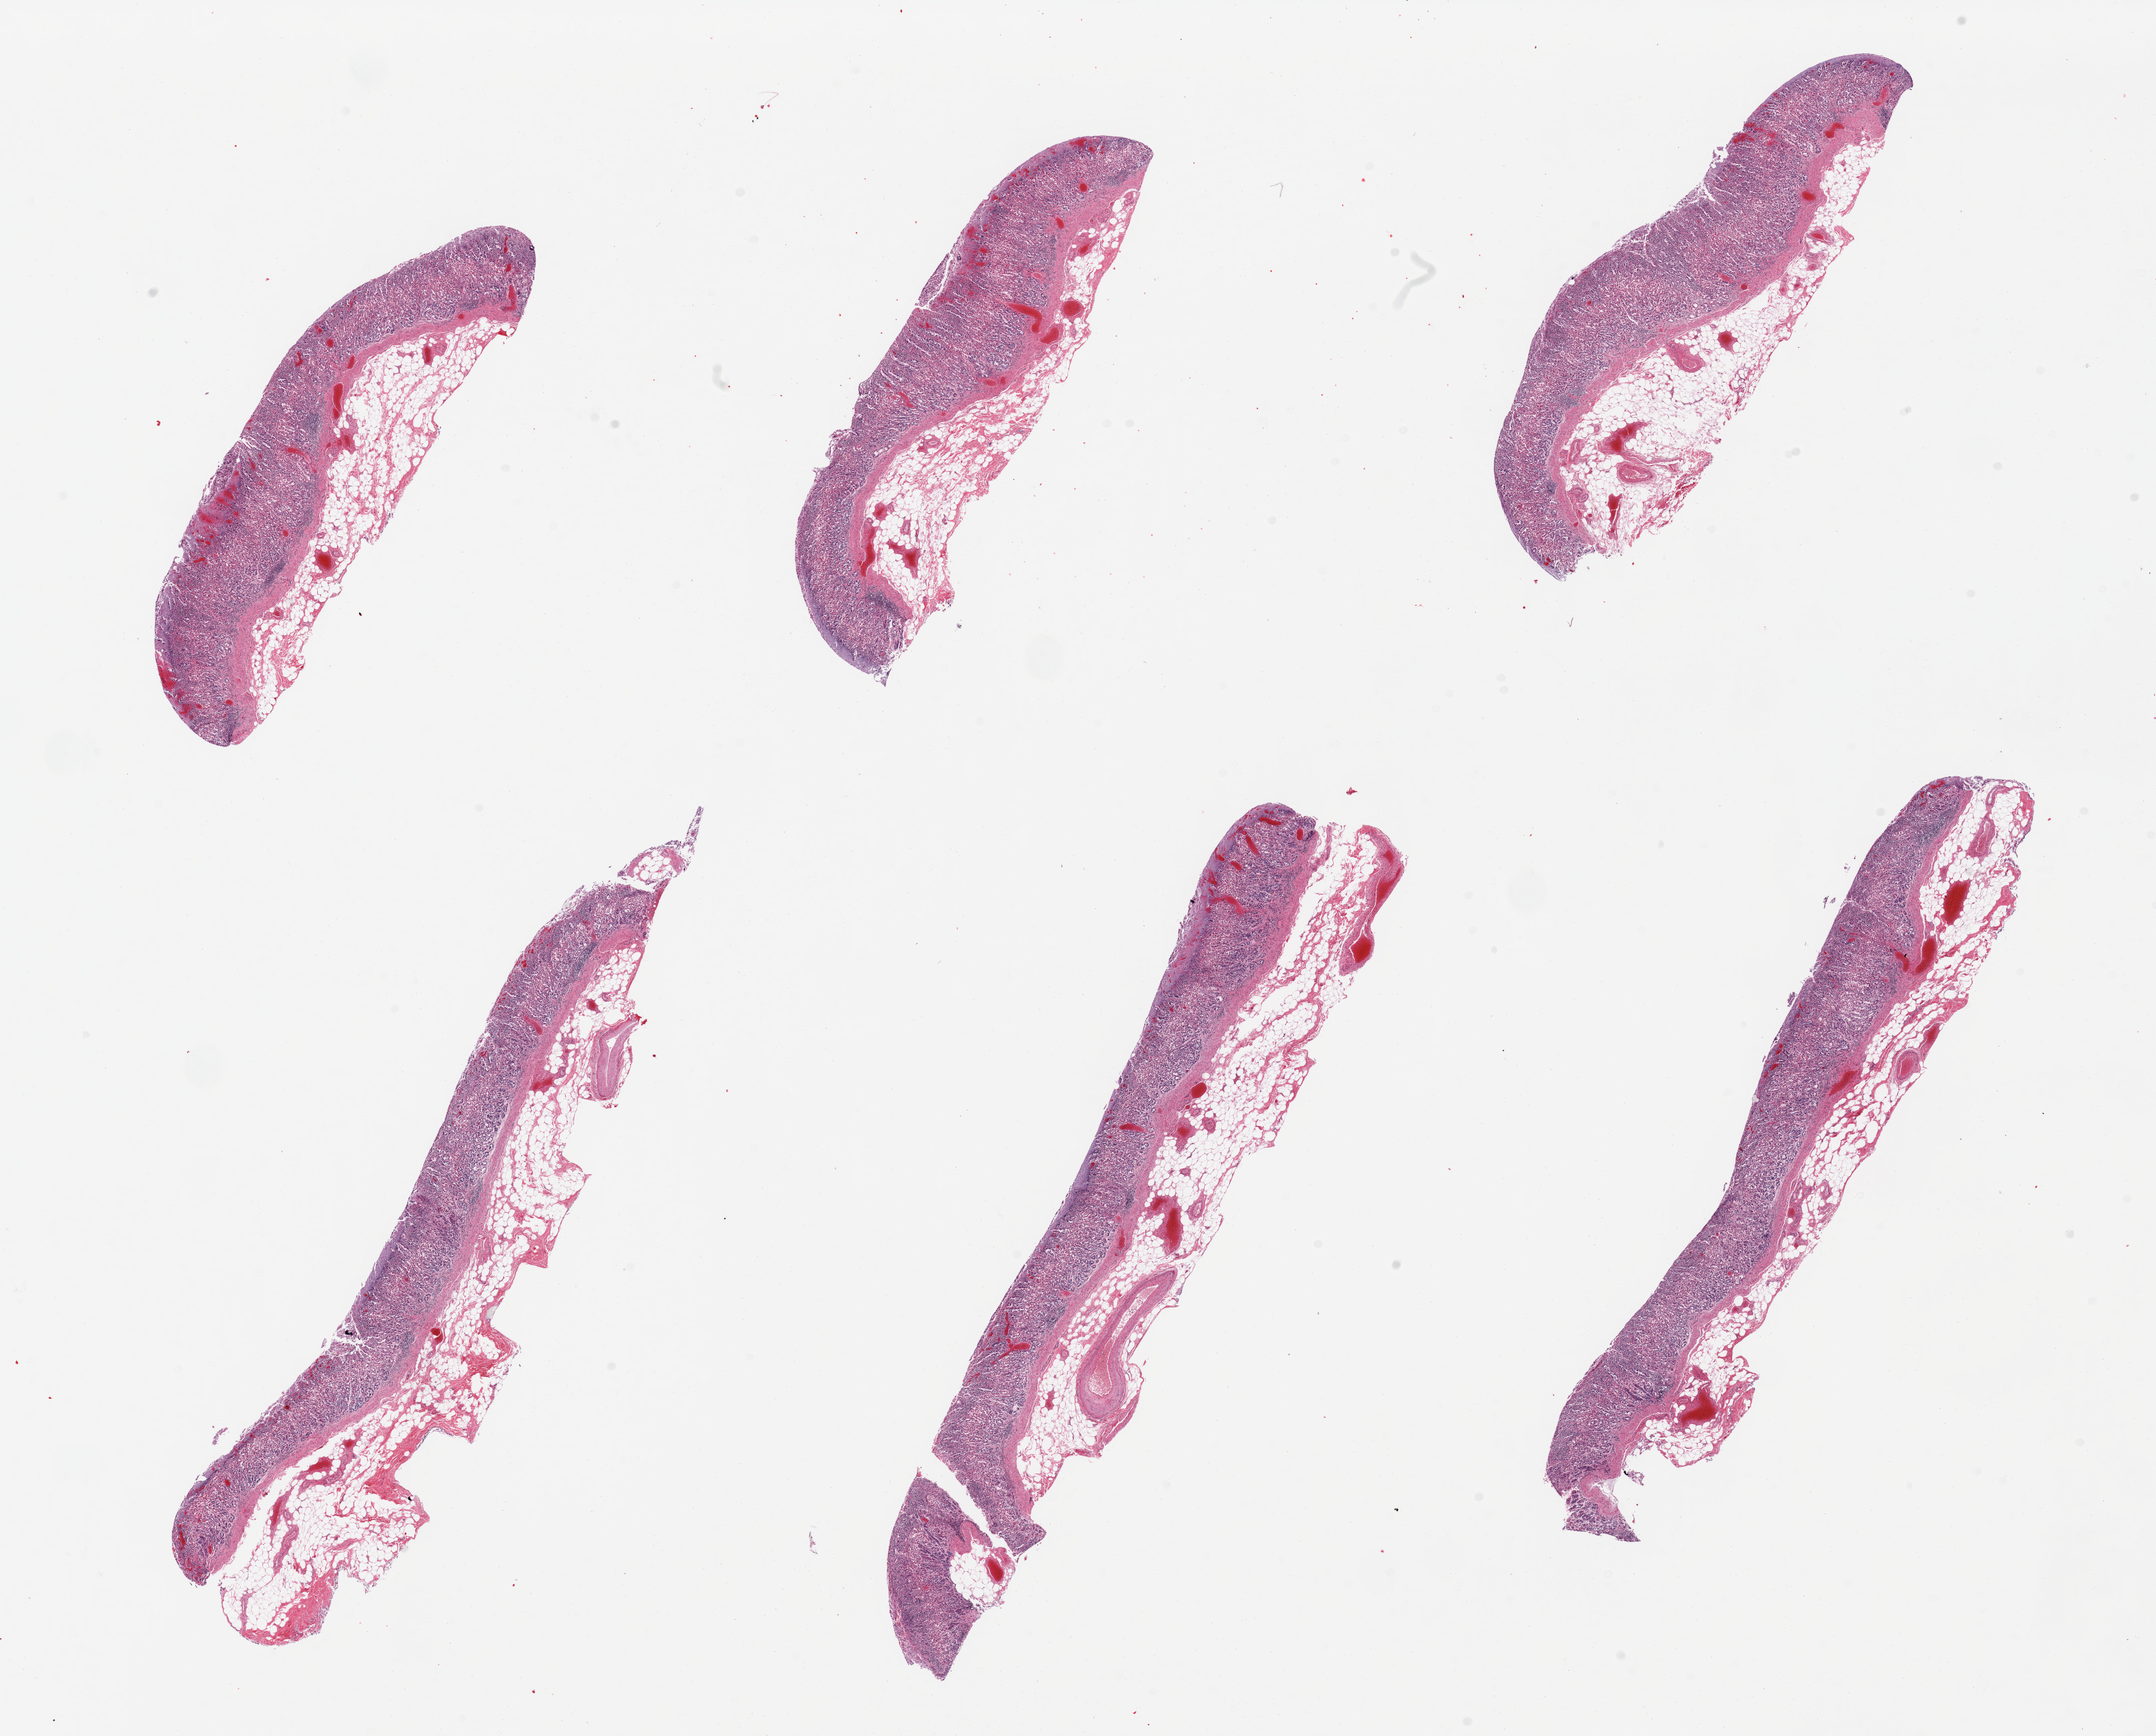
Whole-slide image, H&E stain, shown as a low-resolution overview of the whole scanned area (about 25.6 x 20.6 mm). PAXgene-fixed paraffin-embedded (PFPE) section. Section of stomach (target tissue). Tissue donor sample. Donor sex: male.
Reviewer comment on this tissue sample: 6 pieces; mucosa only.